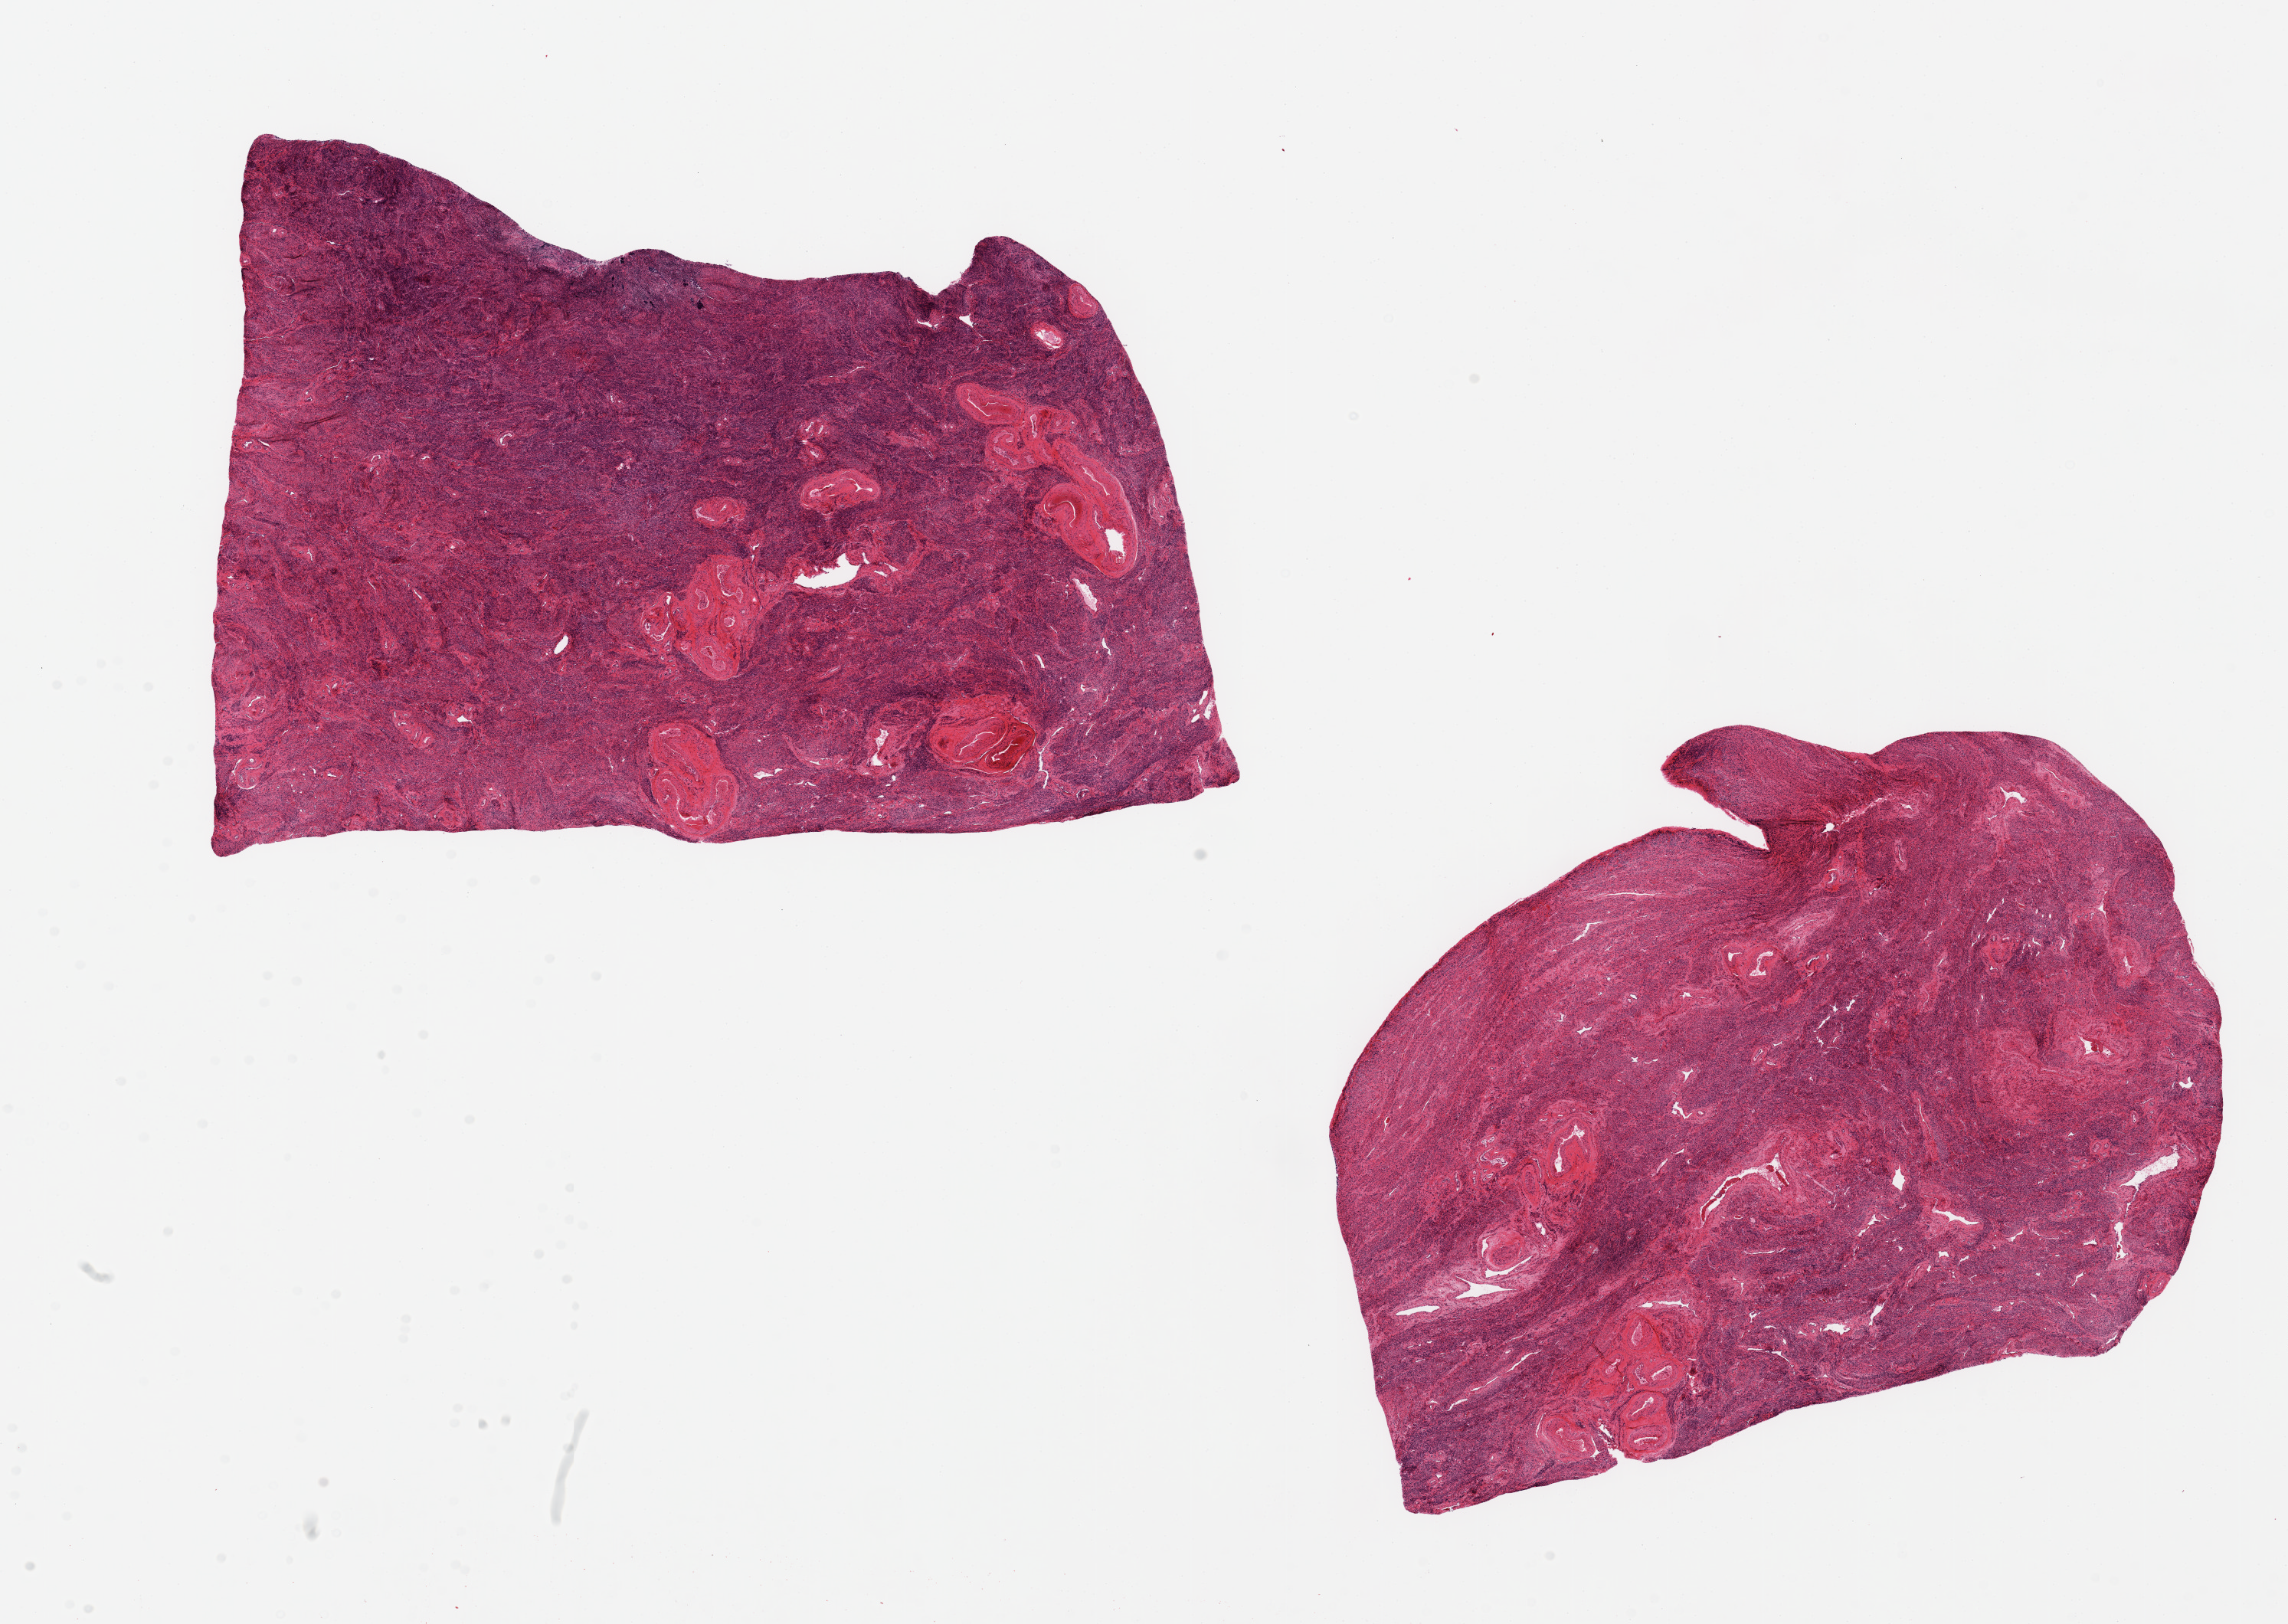
Digitized hematoxylin and eosin (H&E)-stained section, brightfield, whole scanned area (about 23.6 x 16.8 mm, from a 20x scan) shown as a low-resolution overview. PAXgene-fixed, paraffin-embedded tissue. Section of uterus (target tissue). Tissue donor sample. Donor sex: female.
Review note (as recorded): 2 pieces ~10x6mm, no endometrial elements present.